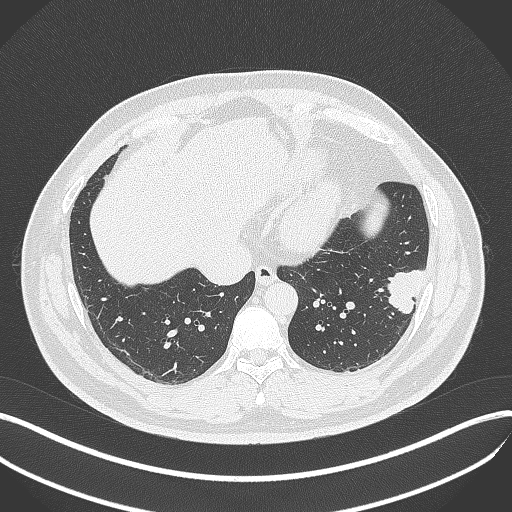
Chest CT, one axial slice. Slice 129 of 429 in the series (ordered by position). Reconstruction kernel B70f. Lung window (W 1500 / L -600 HU). 512 × 512 image matrix. Male patient, age 39 years. Case-level facts recorded for this patient, not image findings: clinical TNM (as recorded): T2a N0 M0.
Structures marked on this image (rectangle marked by the reading radiologist):
- lung tumour (recorded histology: adenocarcinoma): box from (x=384, y=268) to (x=430, y=317) px